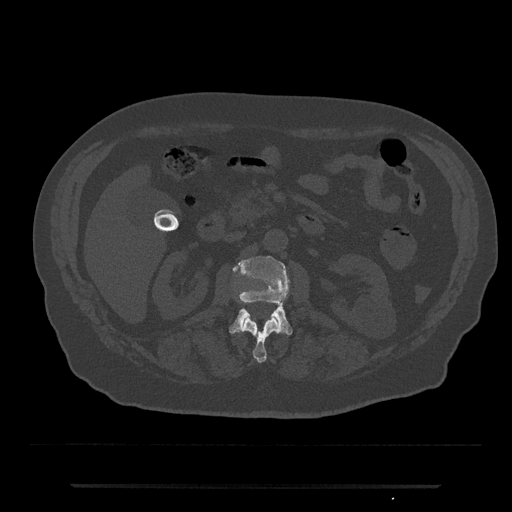
CT including the spine, one axial slice; position 500 of 797 along the scan axis; reconstruction kernel Br40s/3; 120 kVp; bone window (W 1800 / L 400 HU); 0.5 mm slice thickness; 512 × 512 image matrix, field of view 434 × 434 mm. Patient: male, 80 years. Case-level facts recorded for this patient, not image findings: primary cancer: prostate; vertebrae with lytic lesions (as recorded): L1, T11.
Outlined on this slice (semi-automatic segmentation, software-assisted and operator-edited):
- L1 vertebra: bounding box [x1, y1, x2, y2] px = [243, 317, 280, 363]
- L2 vertebra: [229, 256, 293, 335]